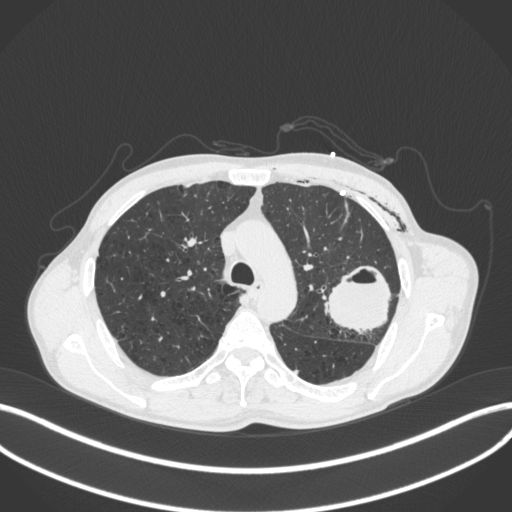
Chest CT, one axial slice. Position 286 of 416 along the scan axis. Reconstruction kernel B31f. Lung window (W 1500 / L -600 HU). 512 × 512 image matrix, field of view 400 × 400 mm. Patient: male, 58 years. Case-level facts recorded for this patient, not image findings: clinical TNM (as recorded): T3 N0 M0.
Outlined on this slice (rectangle marked by the reading radiologist):
- lung tumour (recorded histology: adenocarcinoma): bounding box (x1, y1, x2, y2) in pixels: (325, 265, 398, 335)